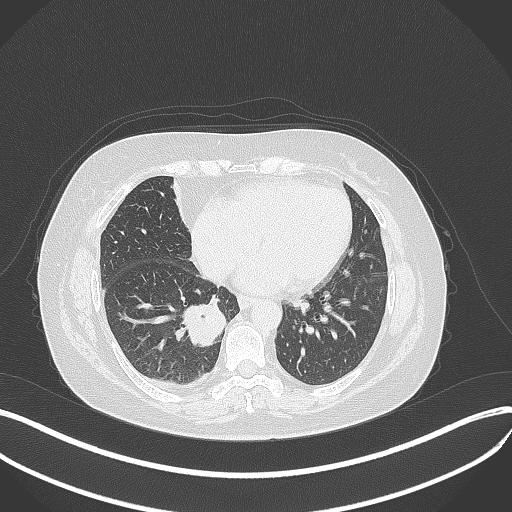
Chest CT, one axial slice; slice 134 of 381 in the series (ordered by position); lung window (W 1500 / L -600 HU); 512 × 512 image matrix. Patient: female, 56 years. From the clinical record (not read from this slice): clinical TNM (as recorded): T2b N1 M0.
Annotated regions visible in this slice (rectangle marked by the reading radiologist):
- lung tumour (recorded histology: small cell carcinoma): bounding box (x1, y1, x2, y2) in pixels: (183, 299, 226, 350)